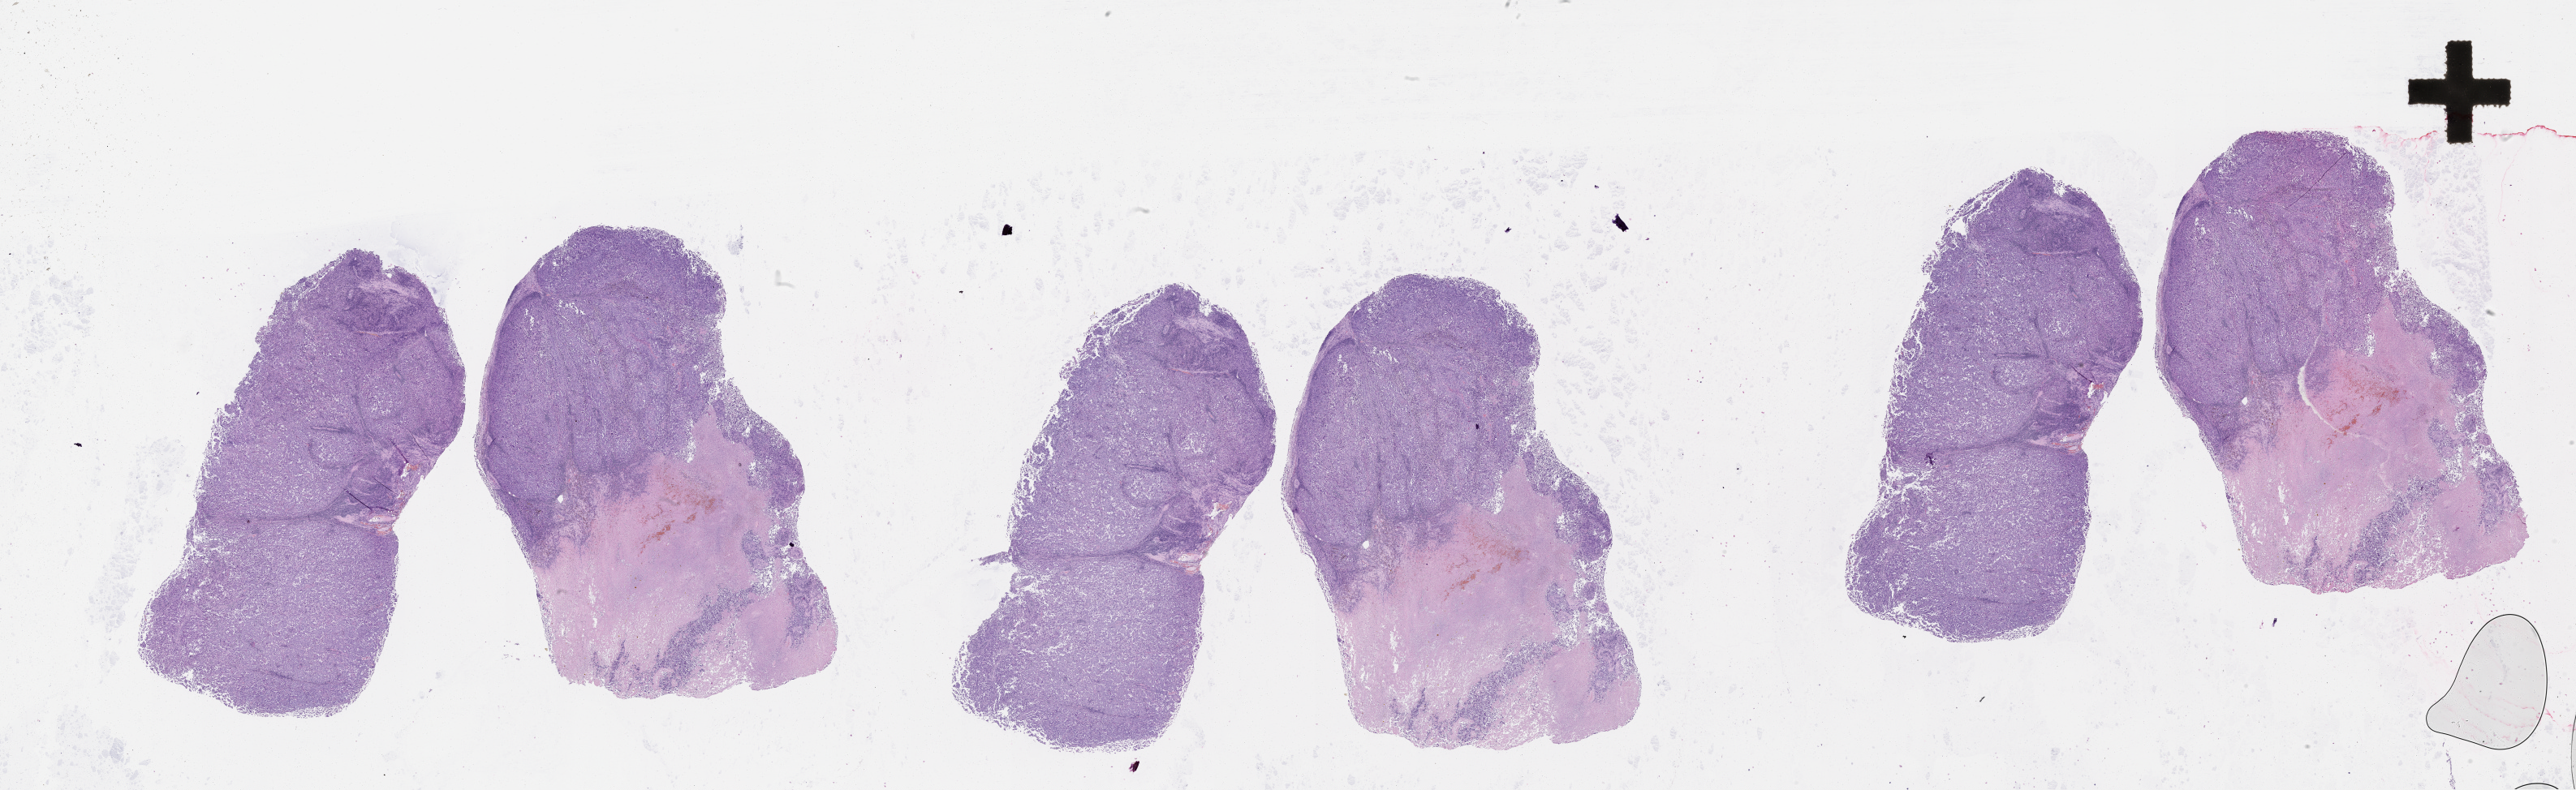
Whole-slide histology image, Hematoxylin and eosin (H&E) stained — whole scanned area (about 51.1 x 15.7 mm, from a 20x scan) shown as a low-resolution overview; tumour tissue sample, sampled site: lymph node. Female, 62 y/o.
This section: metastatic tumour tissue. Patient diagnosis: Malignant melanoma, NOS.